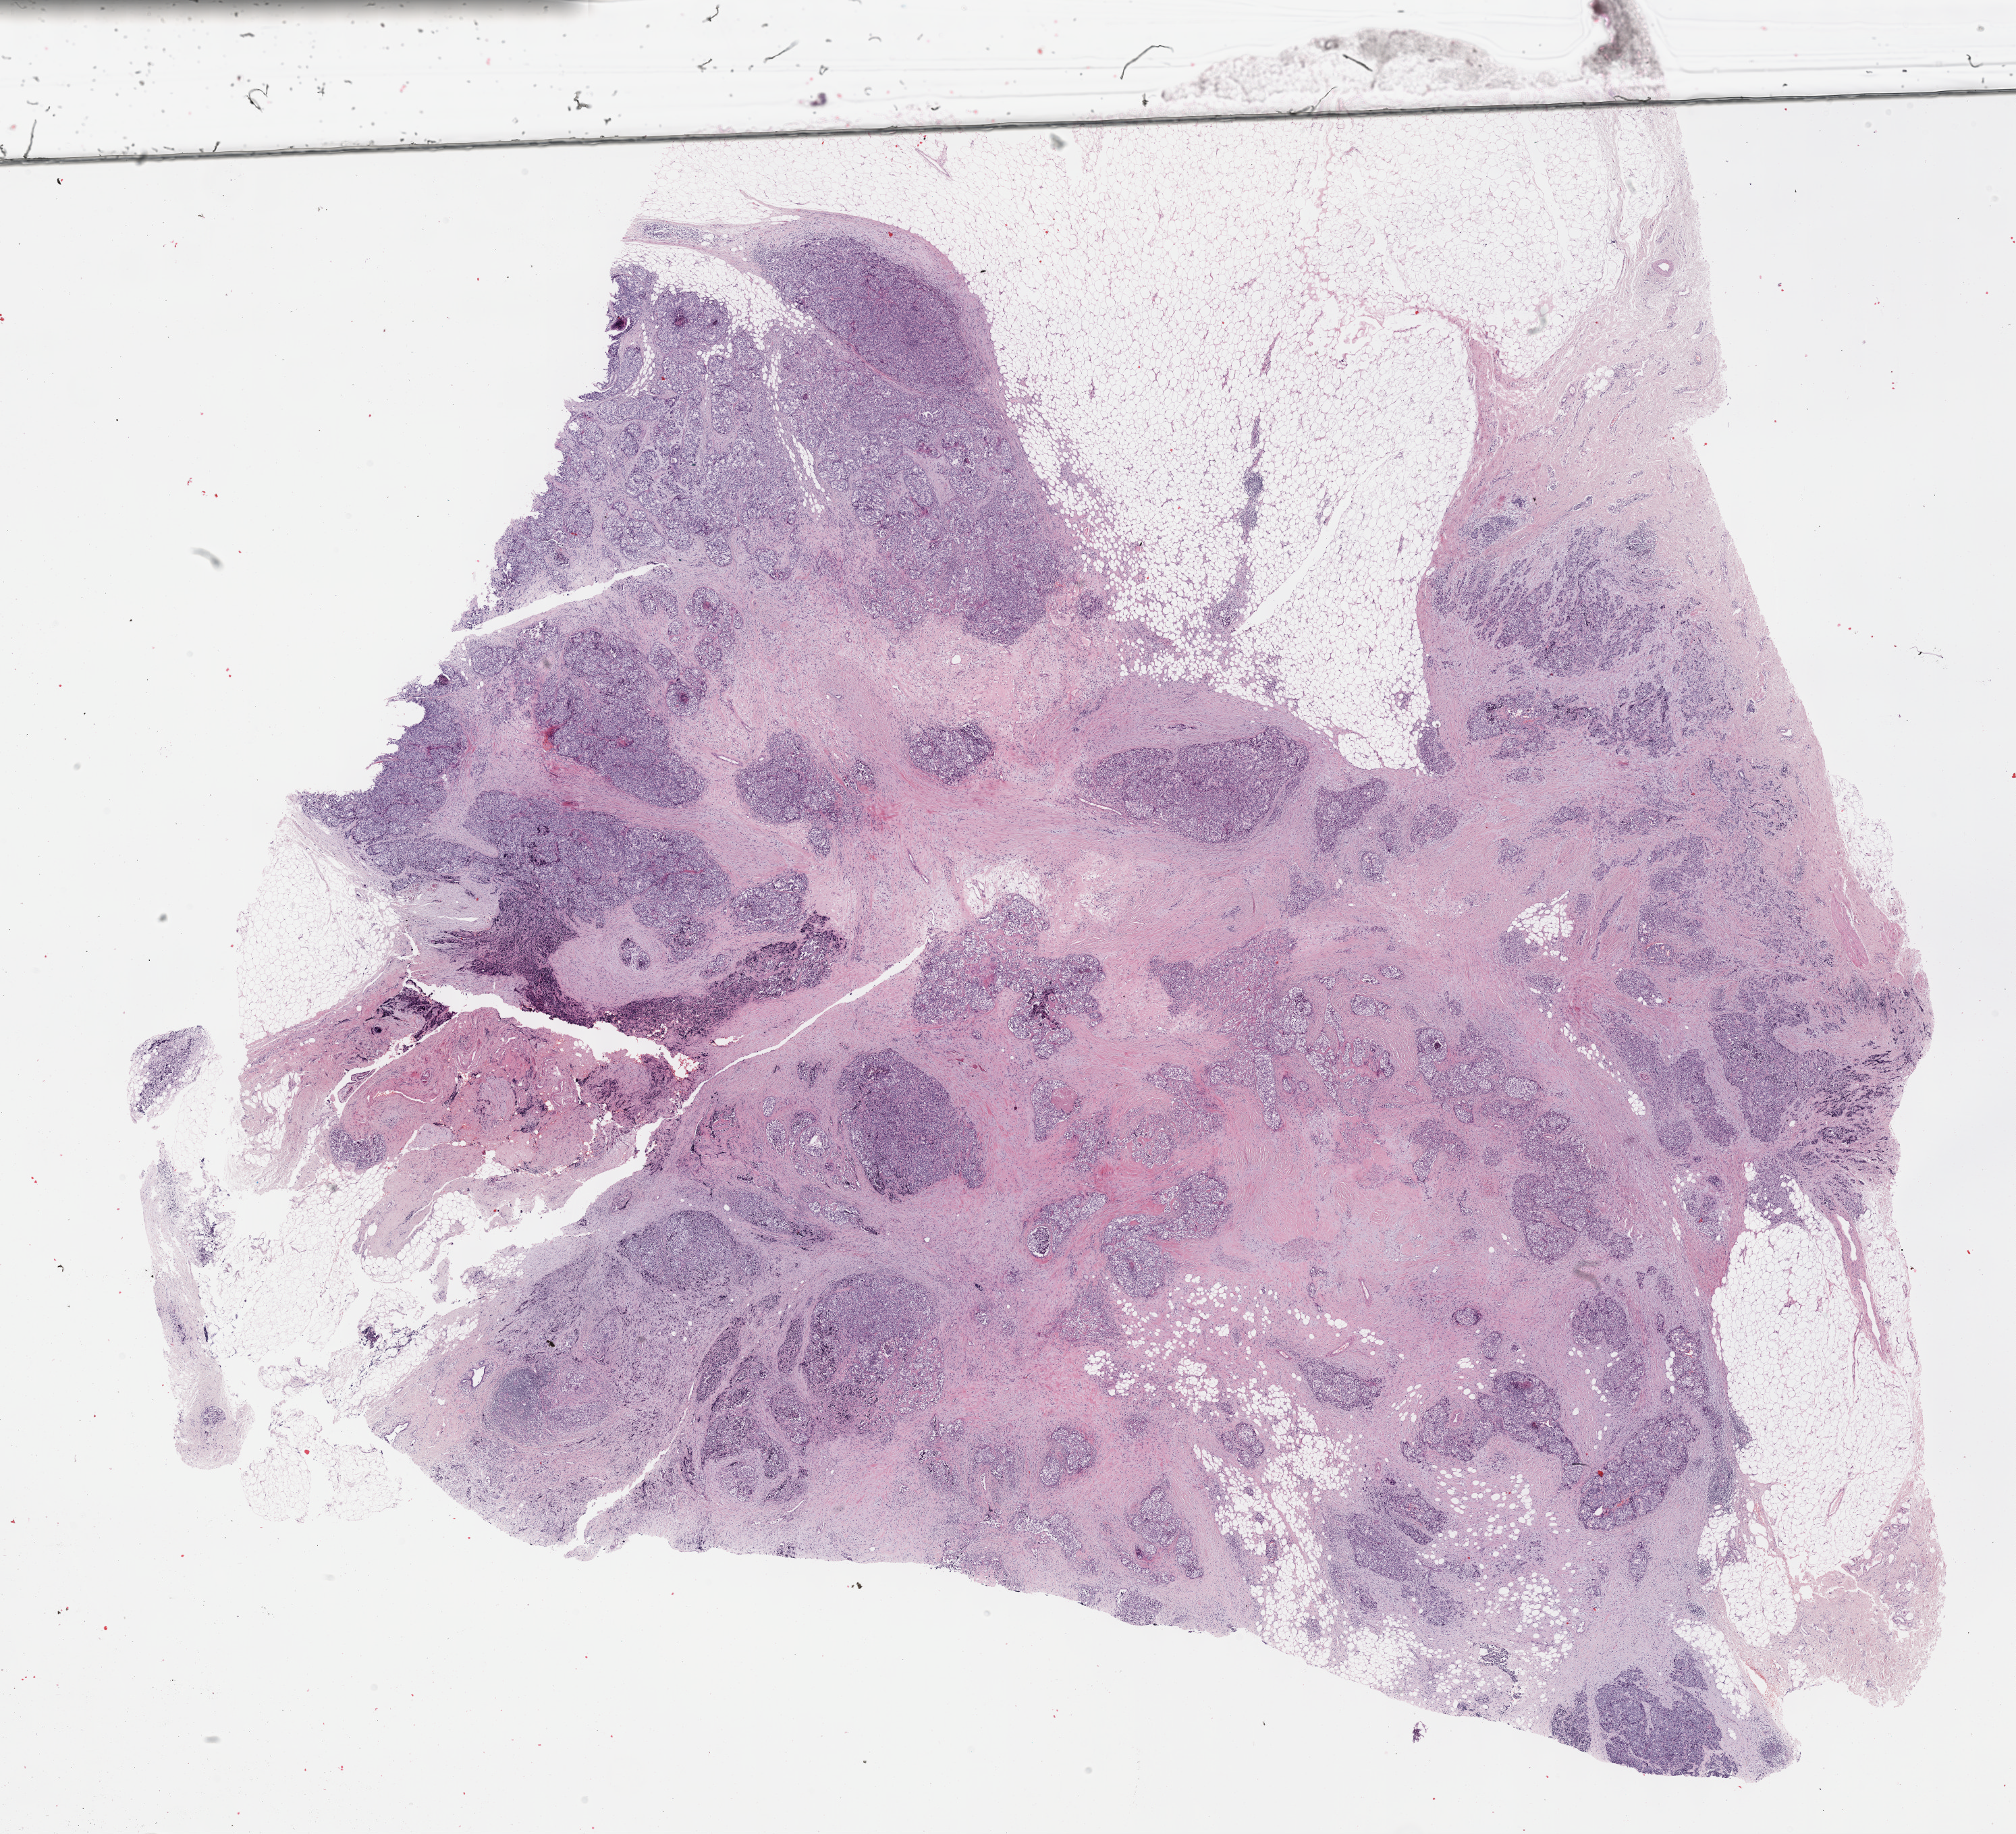
Digitized H&E-stained tissue section (whole slide), shown as a low-resolution overview of the whole scanned area (about 24.2 x 22.0 mm); formalin-fixed paraffin-embedded (FFPE) diagnostic section; sample: primary tumour, breast. Patient: female, age at initial diagnosis 45 years.
• pathologic diagnosis: Infiltrating duct carcinoma, NOS
• AJCC pathologic stage: IIA (7th edition)
• TNM: T2 N0 M0